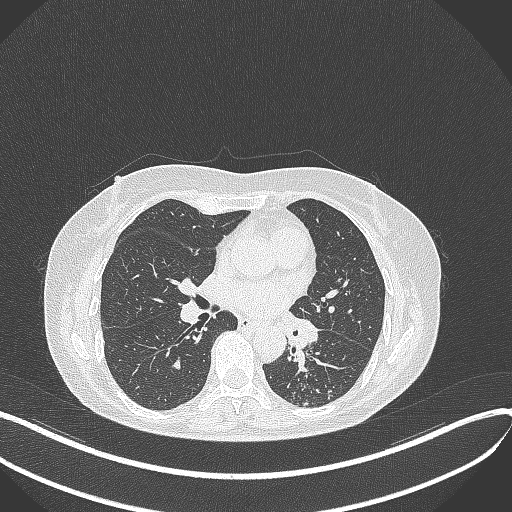
Chest CT, one axial slice; position 211 of 429 along the scan axis; reconstruction kernel B70f; 100 kVp; lung window (W 1500 / L -600 HU); 1 mm slice thickness; 512 × 512 image matrix. Patient: female, 63 years. From the clinical record (not read from this slice): clinical TNM (as recorded): T1b N0 M0; histopathological grade: G2-3.
Annotated regions visible in this slice (rectangle marked by the reading radiologist):
- lung tumour (recorded histology: adenocarcinoma): box from (x=284, y=311) to (x=318, y=356) px